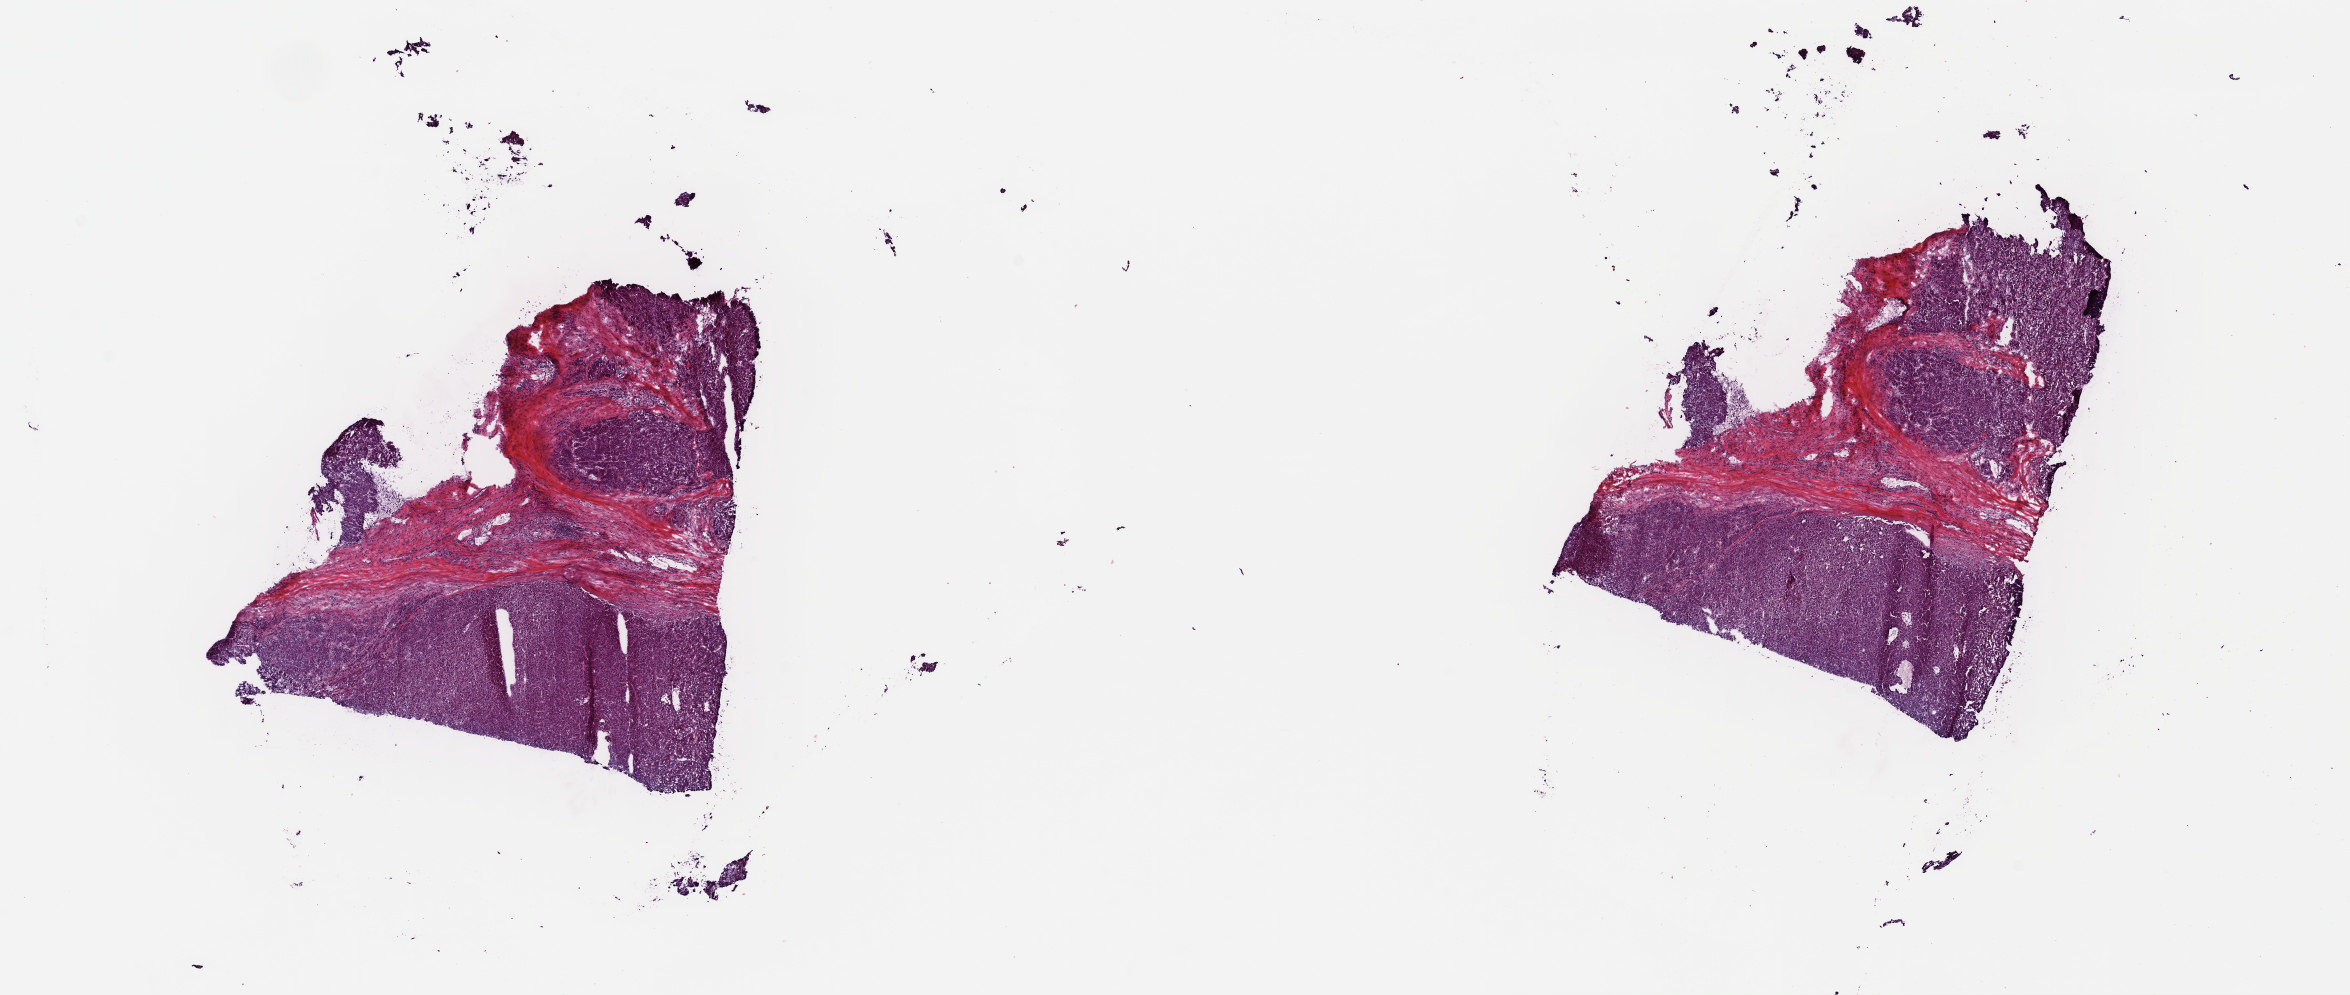
H&E-stained whole-slide image — a low-resolution overview of the entire scanned area, about 18.6 x 7.9 mm (slide scanned at 40x), frozen section from the top of the tissue portion, liver, primary tumour sample. Male, age 77 years at initial diagnosis. Slide review estimates, as recorded: tumour cells 80%, tumour nuclei 80%.
Pathologic diagnosis: Hepatocellular carcinoma, NOS.